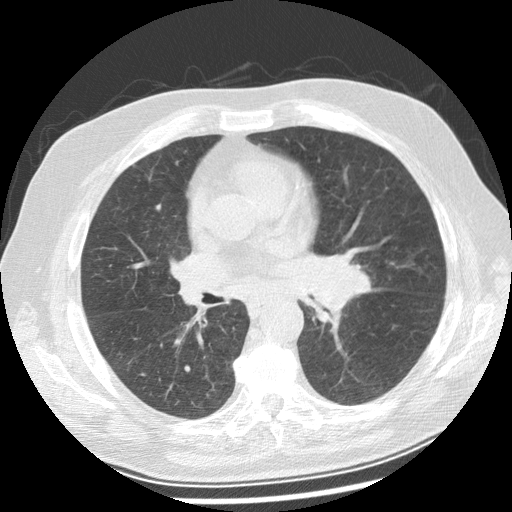
Axial slice from a low-dose chest CT screening exam. Baseline screening round. Lung window (W 1500 / L -600 HU). Slice 115 of 250 in the series. 512 × 512 image matrix. Male, age 70 years at enrolment. Current smoker at enrolment.
Lesion marked by an expert reader, box from (x=288, y=241) to (x=371, y=318) px. Screening reader's record for this exam: no non-calcified nodule ≥4 mm recorded.